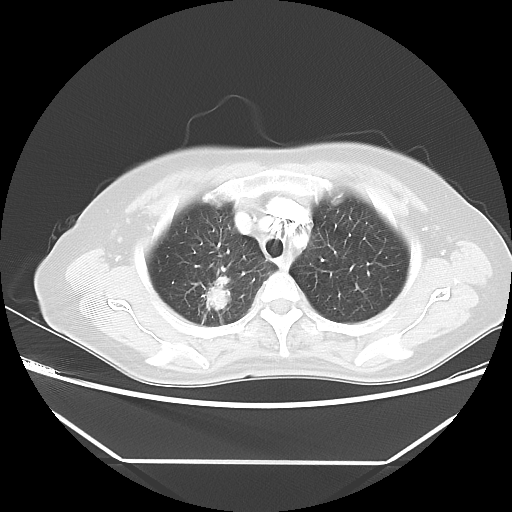
Chest CT, one axial slice; slice 40 of 48 in the series (ordered by position); 100 kVp; lung window (W 1500 / L -600 HU); 512 × 512 image matrix, field of view 360 × 360 mm. Patient: female, 65 years. Case-level facts recorded for this patient, not image findings: clinical TNM (as recorded): T1c N1 M1.
Outlined on this slice (bounding box drawn by a radiologist):
- lung tumour (recorded histology: adenocarcinoma): box from (x=198, y=268) to (x=239, y=319) px